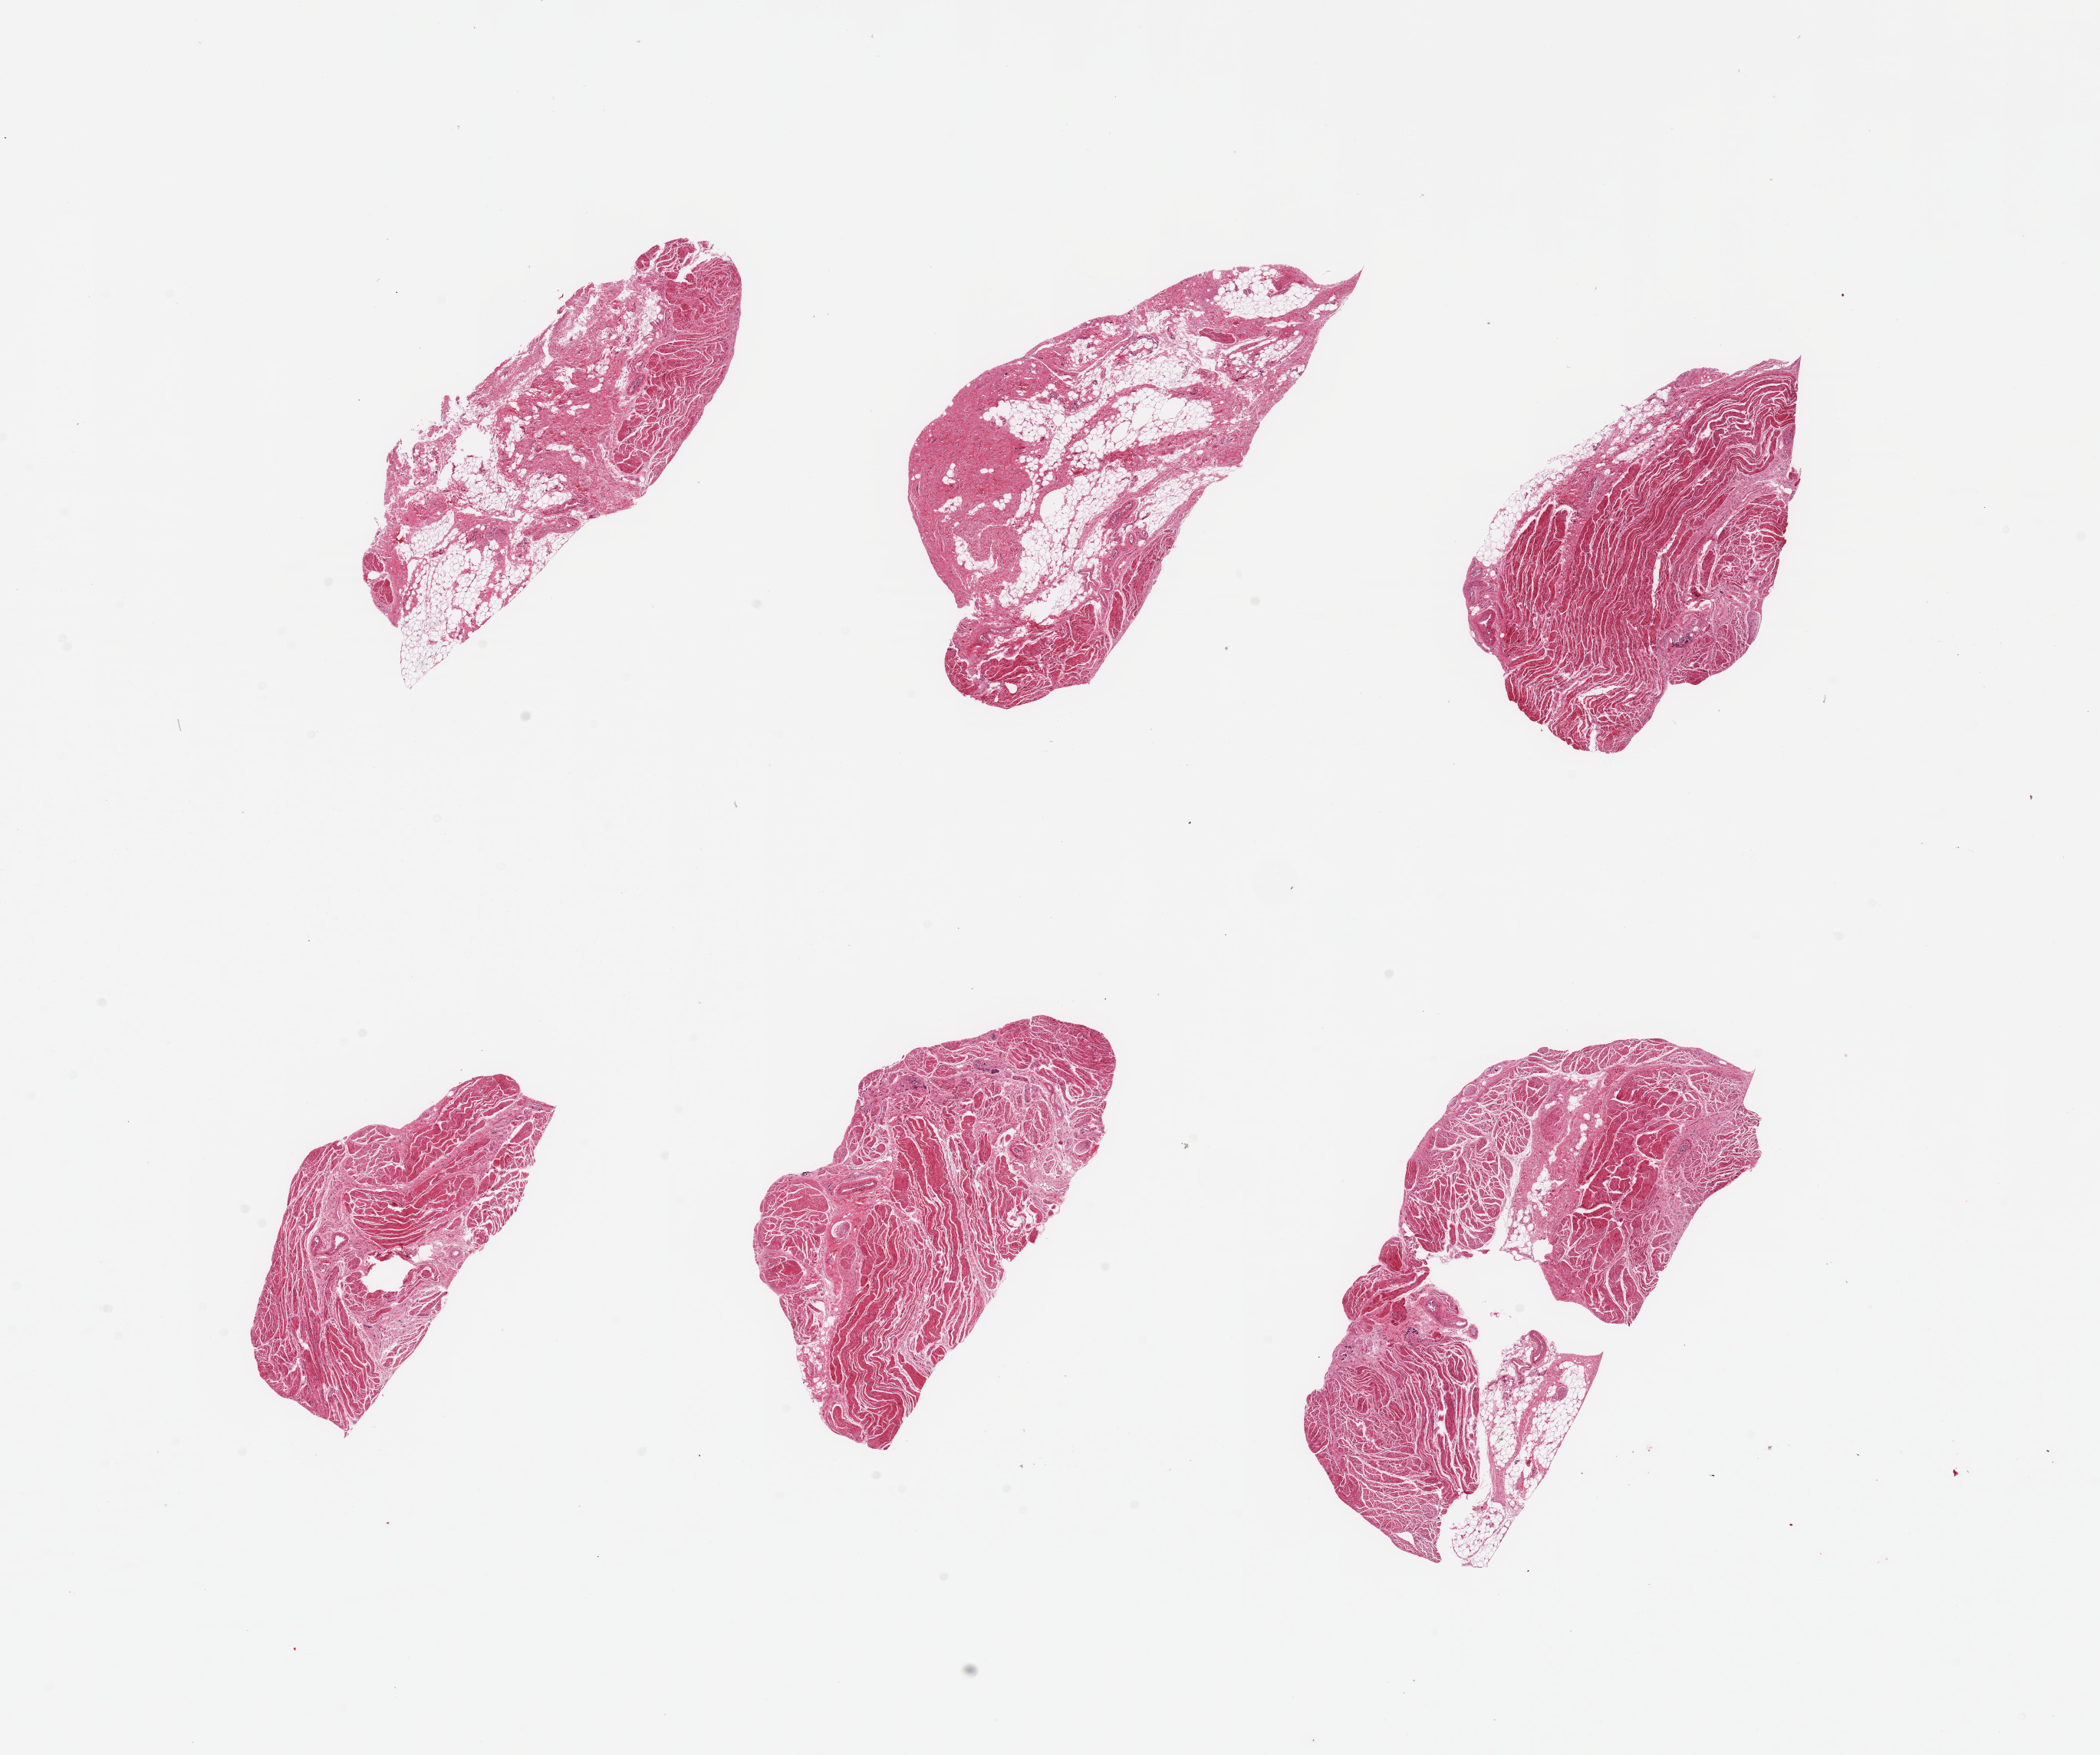
Digitized H&E-stained section, a low-resolution overview of the entire scanned area, about 21.7 x 18.1 mm; PAXgene-fixed paraffin-embedded (PFPE) section; target tissue: gastroesophageal junction; donor tissue sample. Donor: male.
Reviewer comment on this tissue sample: 6 pieces, target muscularis is ~65% of tissue.